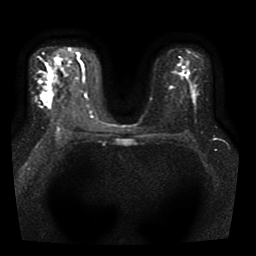
Breast MRI, one axial slice; slice 27 of 41 in the series (ordered by position); diffusion-weighted series; image 2 of 4 stored at this slice position (different b-values; order by instance number); 1.5 T; 5 mm slice thickness; 256 × 256 image matrix, field of view 330 × 330 mm. Female patient.
Outlined on this slice (expert manual segmentation):
- tumour on diffusion-weighted imaging: bounding box [x1, y1, x2, y2] px = [46, 95, 50, 100]